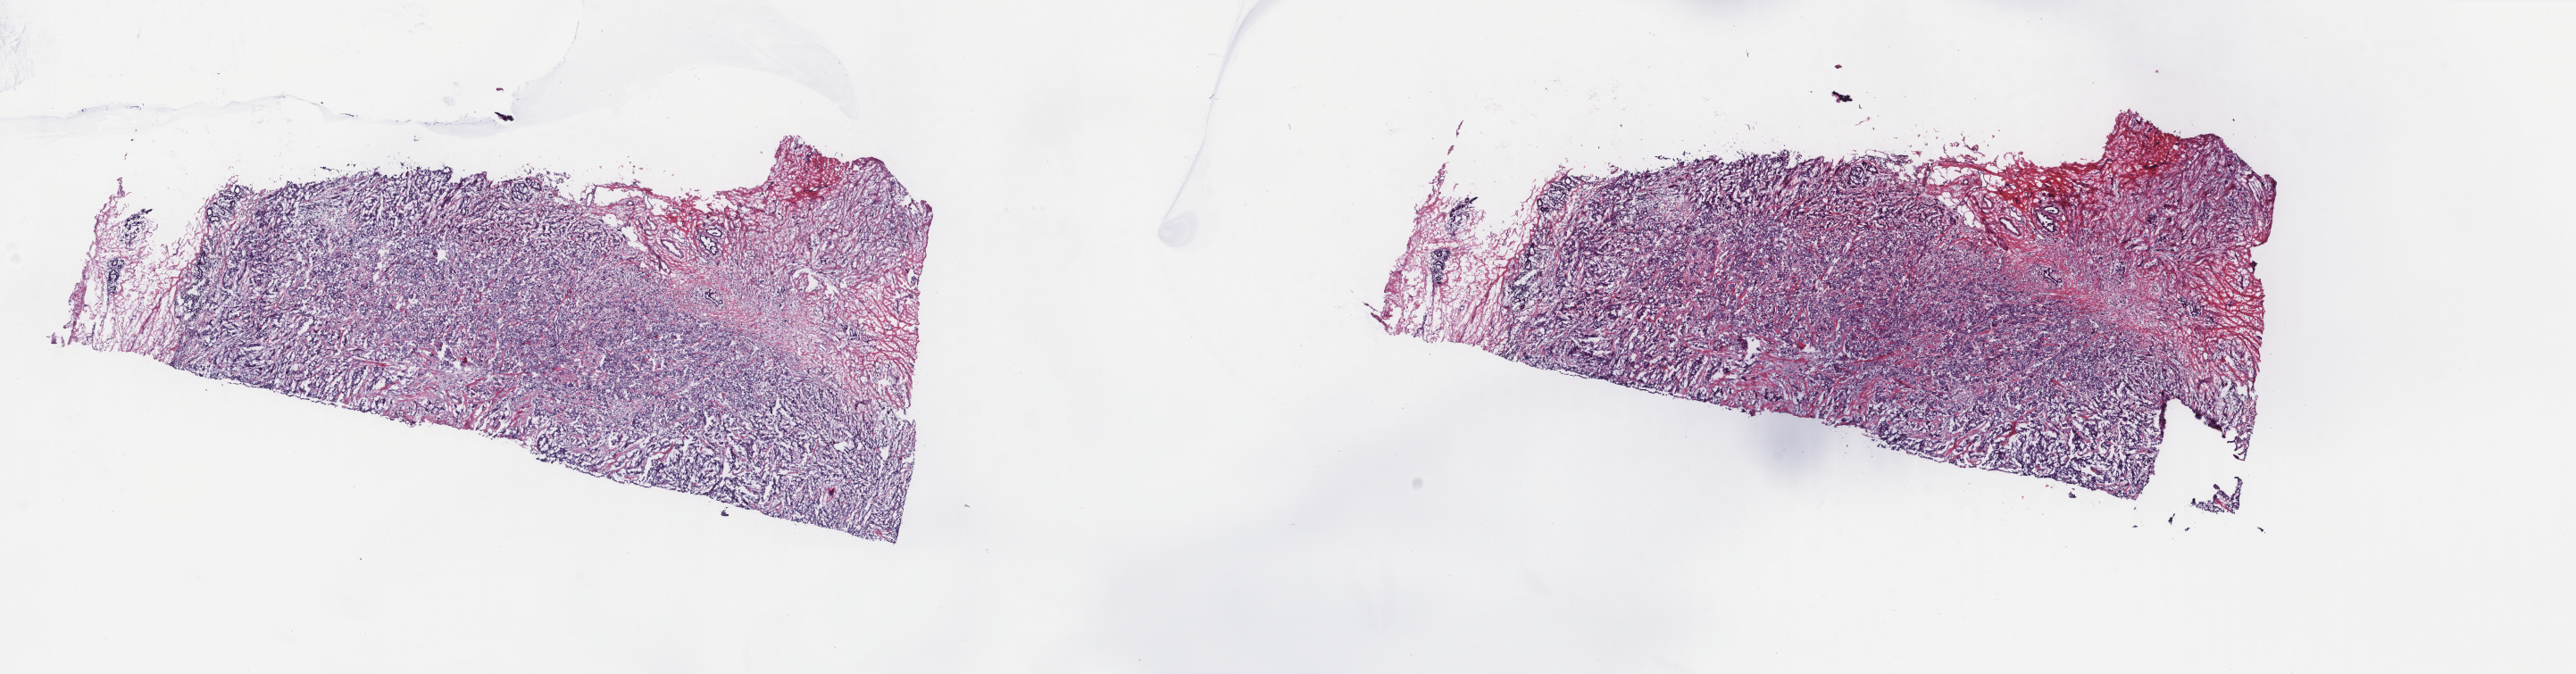
Whole-slide histology image, Hematoxylin and eosin (H&E) stained, shown as a low-resolution overview of the whole scanned area (about 22.9 x 6.0 mm, slide scanned at 40x), frozen section from the top of the tissue portion, primary tumour sample from the breast. Female, age 80 years at initial diagnosis. Composition of this section per pathologist review: tumour cells 95%, tumour nuclei 90%, normal cells 5%, stromal cells 0%, necrosis 0%. Inflammatory infiltration, as recorded: lymphocyte infiltration 0%, monocyte infiltration 0%, neutrophil infiltration 0%.
AJCC pathologic stage: I. Diagnosis: Infiltrating duct carcinoma, NOS. Laterality: left.